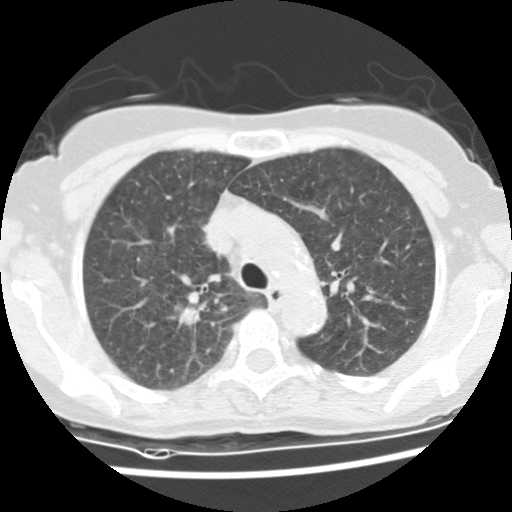
Low-dose screening chest CT, one axial slice; slice 101 of 134 in the series (ordered by position); reconstruction kernel STANDARD; 120 kVp; lung window (W 1500 / L -600 HU); 2.5 mm slice thickness; 512 × 512 image matrix.
Outlined on this slice (expert manual segmentation):
- lesion 1 (tumor, upper lobe of right lung): bounding box (x1, y1, x2, y2) in pixels: (176, 305, 201, 328)